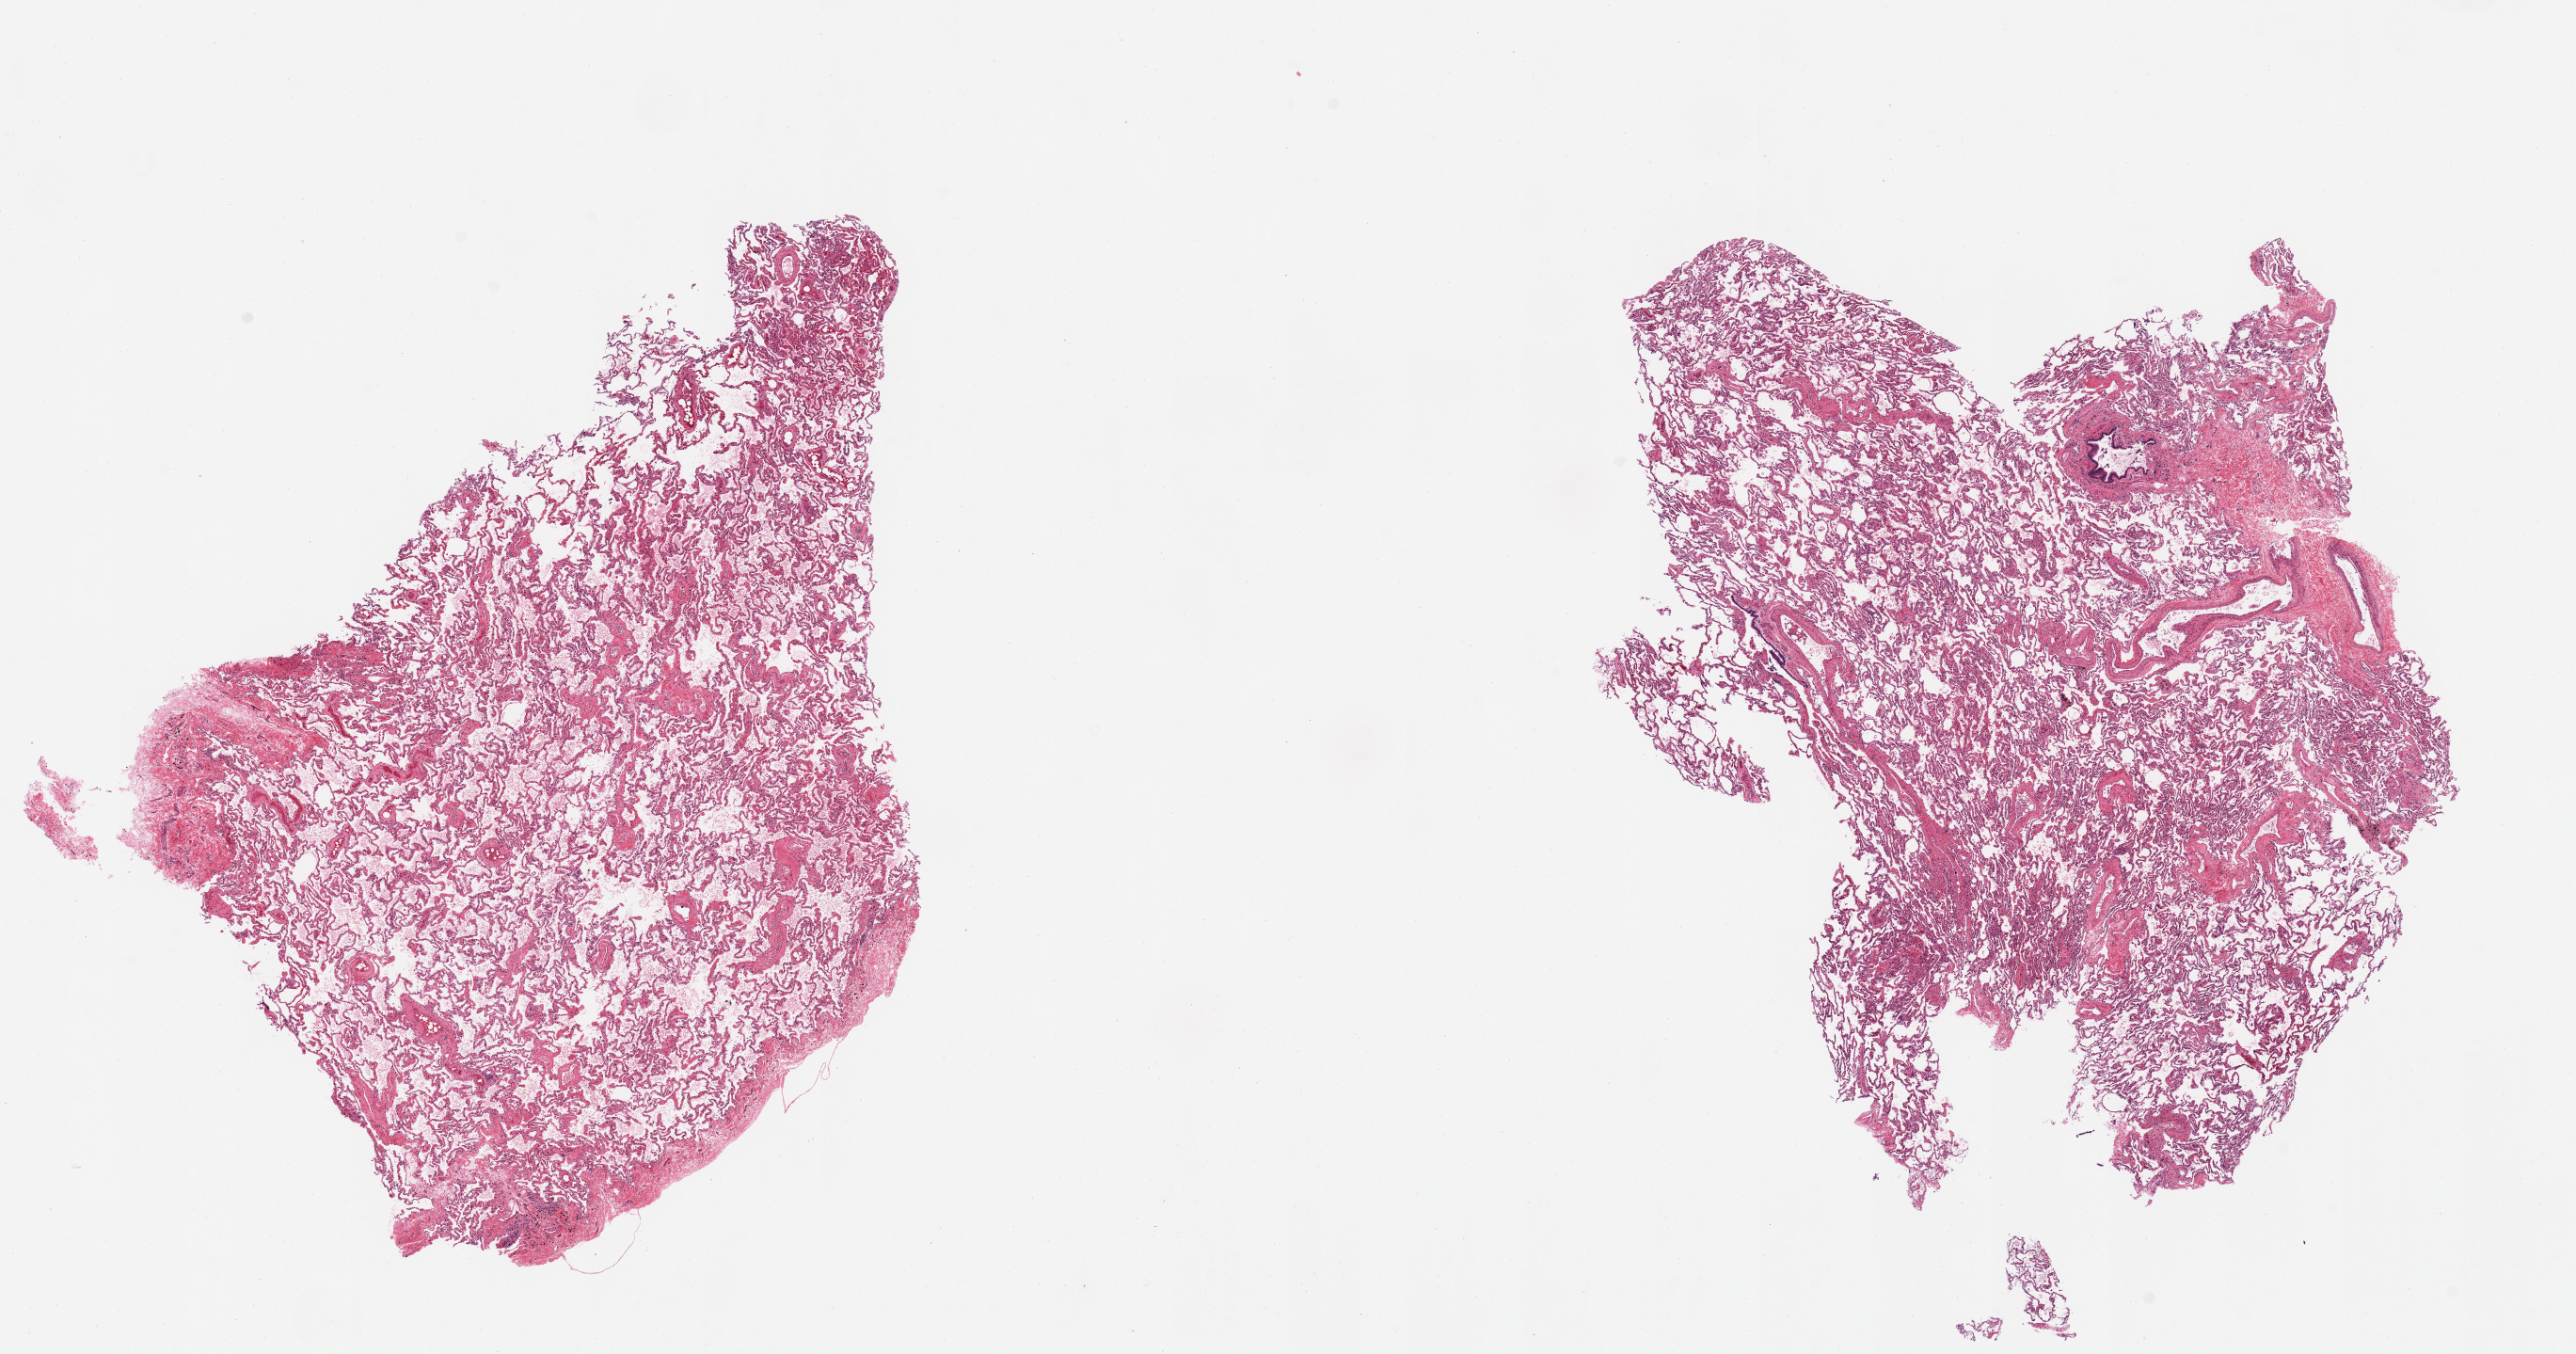
Whole-slide image, hematoxylin and eosin (H&E) stain — whole scanned area (about 21.7 x 11.4 mm, slide scanned at 20x) shown as a low-resolution overview, PAXgene-fixed paraffin-embedded (PFPE) section, section of lung (target tissue), donor tissue sample. Donor: male.
• review note (as recorded): 2 pieces